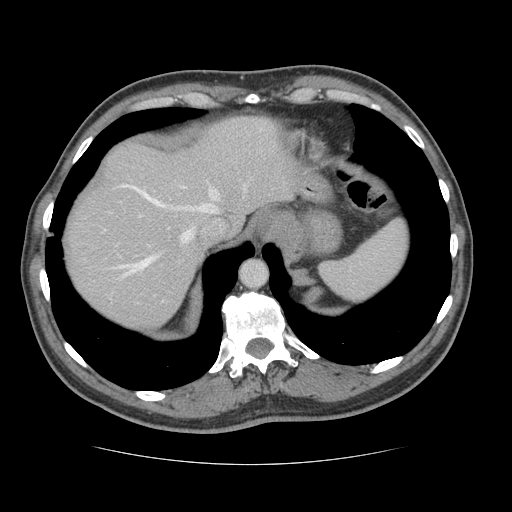
Contrast-enhanced abdominal CT, one axial slice. Position 108 of 134 along the scan axis. Intravenous contrast given. Soft-tissue window (W 400 / L 40 HU). 2.5 mm slice thickness. 512 × 512 image matrix, field of view 377 × 377 mm. Male patient, age 68 years. Case-level facts recorded for this patient, not image findings: diagnosis: colorectal cancer liver metastases, imaged before liver resection.
Outlined on this slice (expert manual segmentation):
- hepatic veins: bounding box (x1, y1, x2, y2) in pixels: (119, 184, 246, 274)
- liver: (66, 117, 290, 328)
- planned liver remnant (the part of the liver to remain after resection): (66, 117, 290, 313)